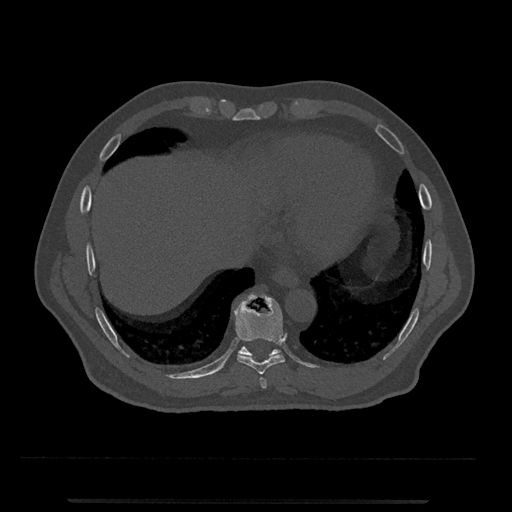
CT including the spine, one axial slice; position 558 of 797 along the scan axis; bone window (W 1800 / L 400 HU); 512 × 512 image matrix, field of view 419 × 419 mm. Patient: male, 63 years. From the clinical record (not read from this slice): primary cancer: prostate.
Outlined on this slice (semi-automatic segmentation, software-assisted and operator-edited):
- T10 vertebra: bounding box <238,346,281,358> (left, top, right, bottom; pixels)
- T8 vertebra: <259,377,267,389>
- T9 vertebra: <235,293,285,375>